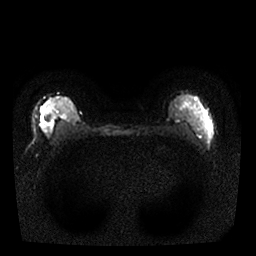
Breast MRI, one axial slice; slice 13 of 25 in the series (ordered by position); diffusion-weighted series; image 2 of 4 stored at this slice position (different b-values; order by instance number); 1.5 T; 4 mm slice thickness; 256 × 256 image matrix, field of view 310 × 310 mm. Female patient.
Structures marked on this image (manually delineated by an expert):
- tumour on diffusion-weighted imaging: bounding box [x1, y1, x2, y2] px = [41, 114, 45, 128]